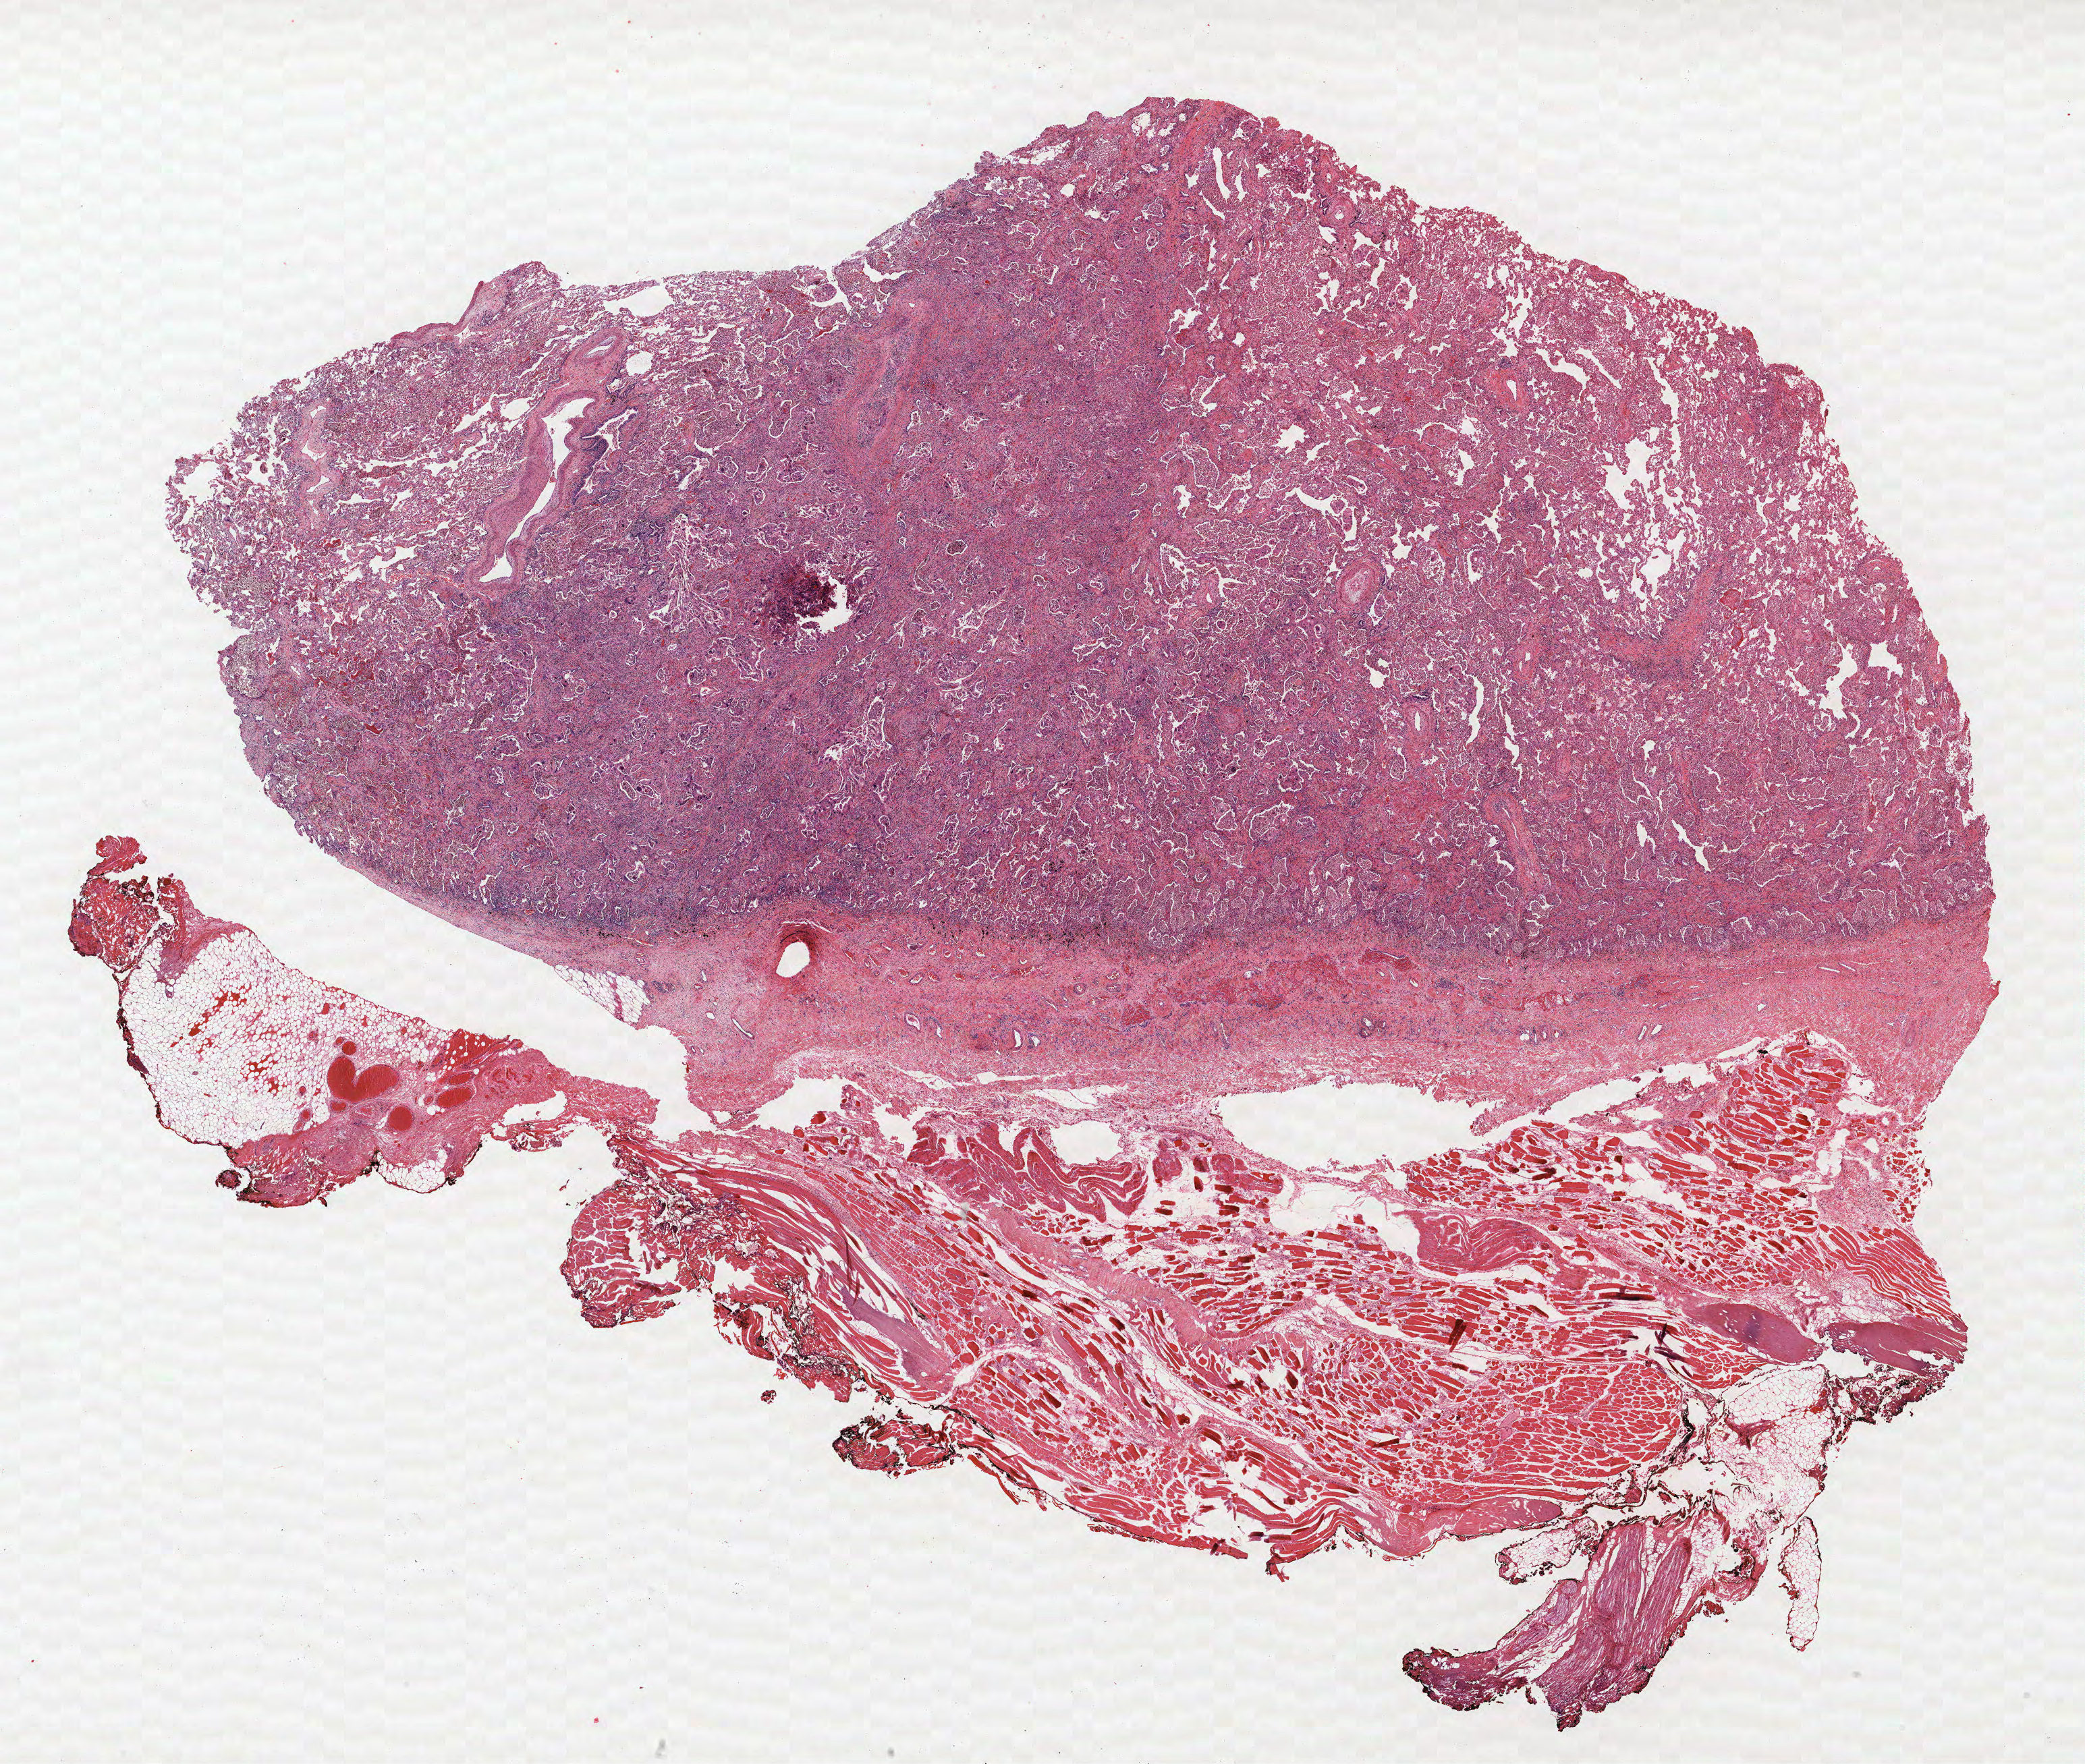
Hematoxylin and eosin (H&E) stained whole-slide image — whole scanned area (about 24.7 x 20.9 mm, from a 40x scan) shown as a low-resolution overview; formalin-fixed paraffin-embedded (FFPE) section; lung. Female patient, aged 57 at enrolment. Current smoker at enrolment. Grade: poorly differentiated (G3).
Tumour size (pathology): 60 mm. Primary tumour location (clinical record): right upper lobe. Stage (AJCC 6th edition): IIIA. Participant's lung-cancer diagnosis: Adenosquamous carcinoma (ICD-O-3 8560/3).